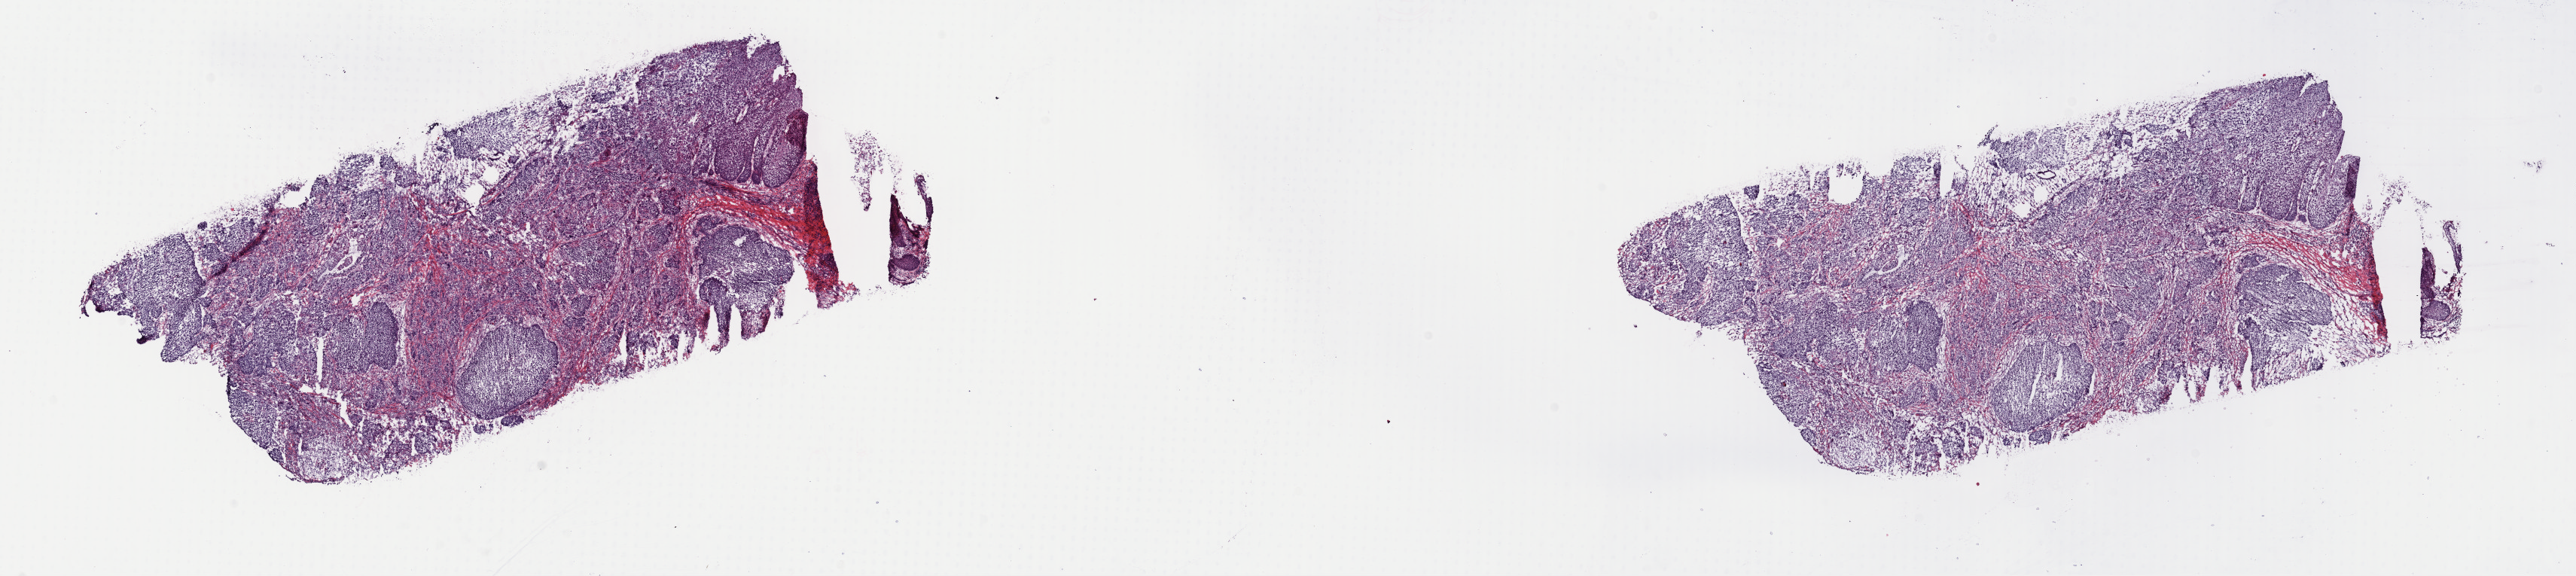
Digitized H&E-stained tissue section (whole slide) — a low-resolution overview of the entire scanned area, about 27.0 x 6.0 mm (slide scanned at 40x). Frozen section from the top of the tissue portion. Primary tumour sample from the head and neck. Male, age 56 years at initial diagnosis. Histologic grade: G2 (moderately differentiated). Composition of this section per pathologist review: tumour cells 80%, tumour nuclei 80%, normal cells 0%, stromal cells 20%, necrosis 0%. Infiltration values recorded for this section: lymphocyte infiltration 0%, monocyte infiltration 0%, neutrophil infiltration 0%.
TNM: T2 N1 M0. Histologic diagnosis: Squamous cell carcinoma, NOS (anterior floor of mouth). AJCC pathologic stage: III (7th edition).